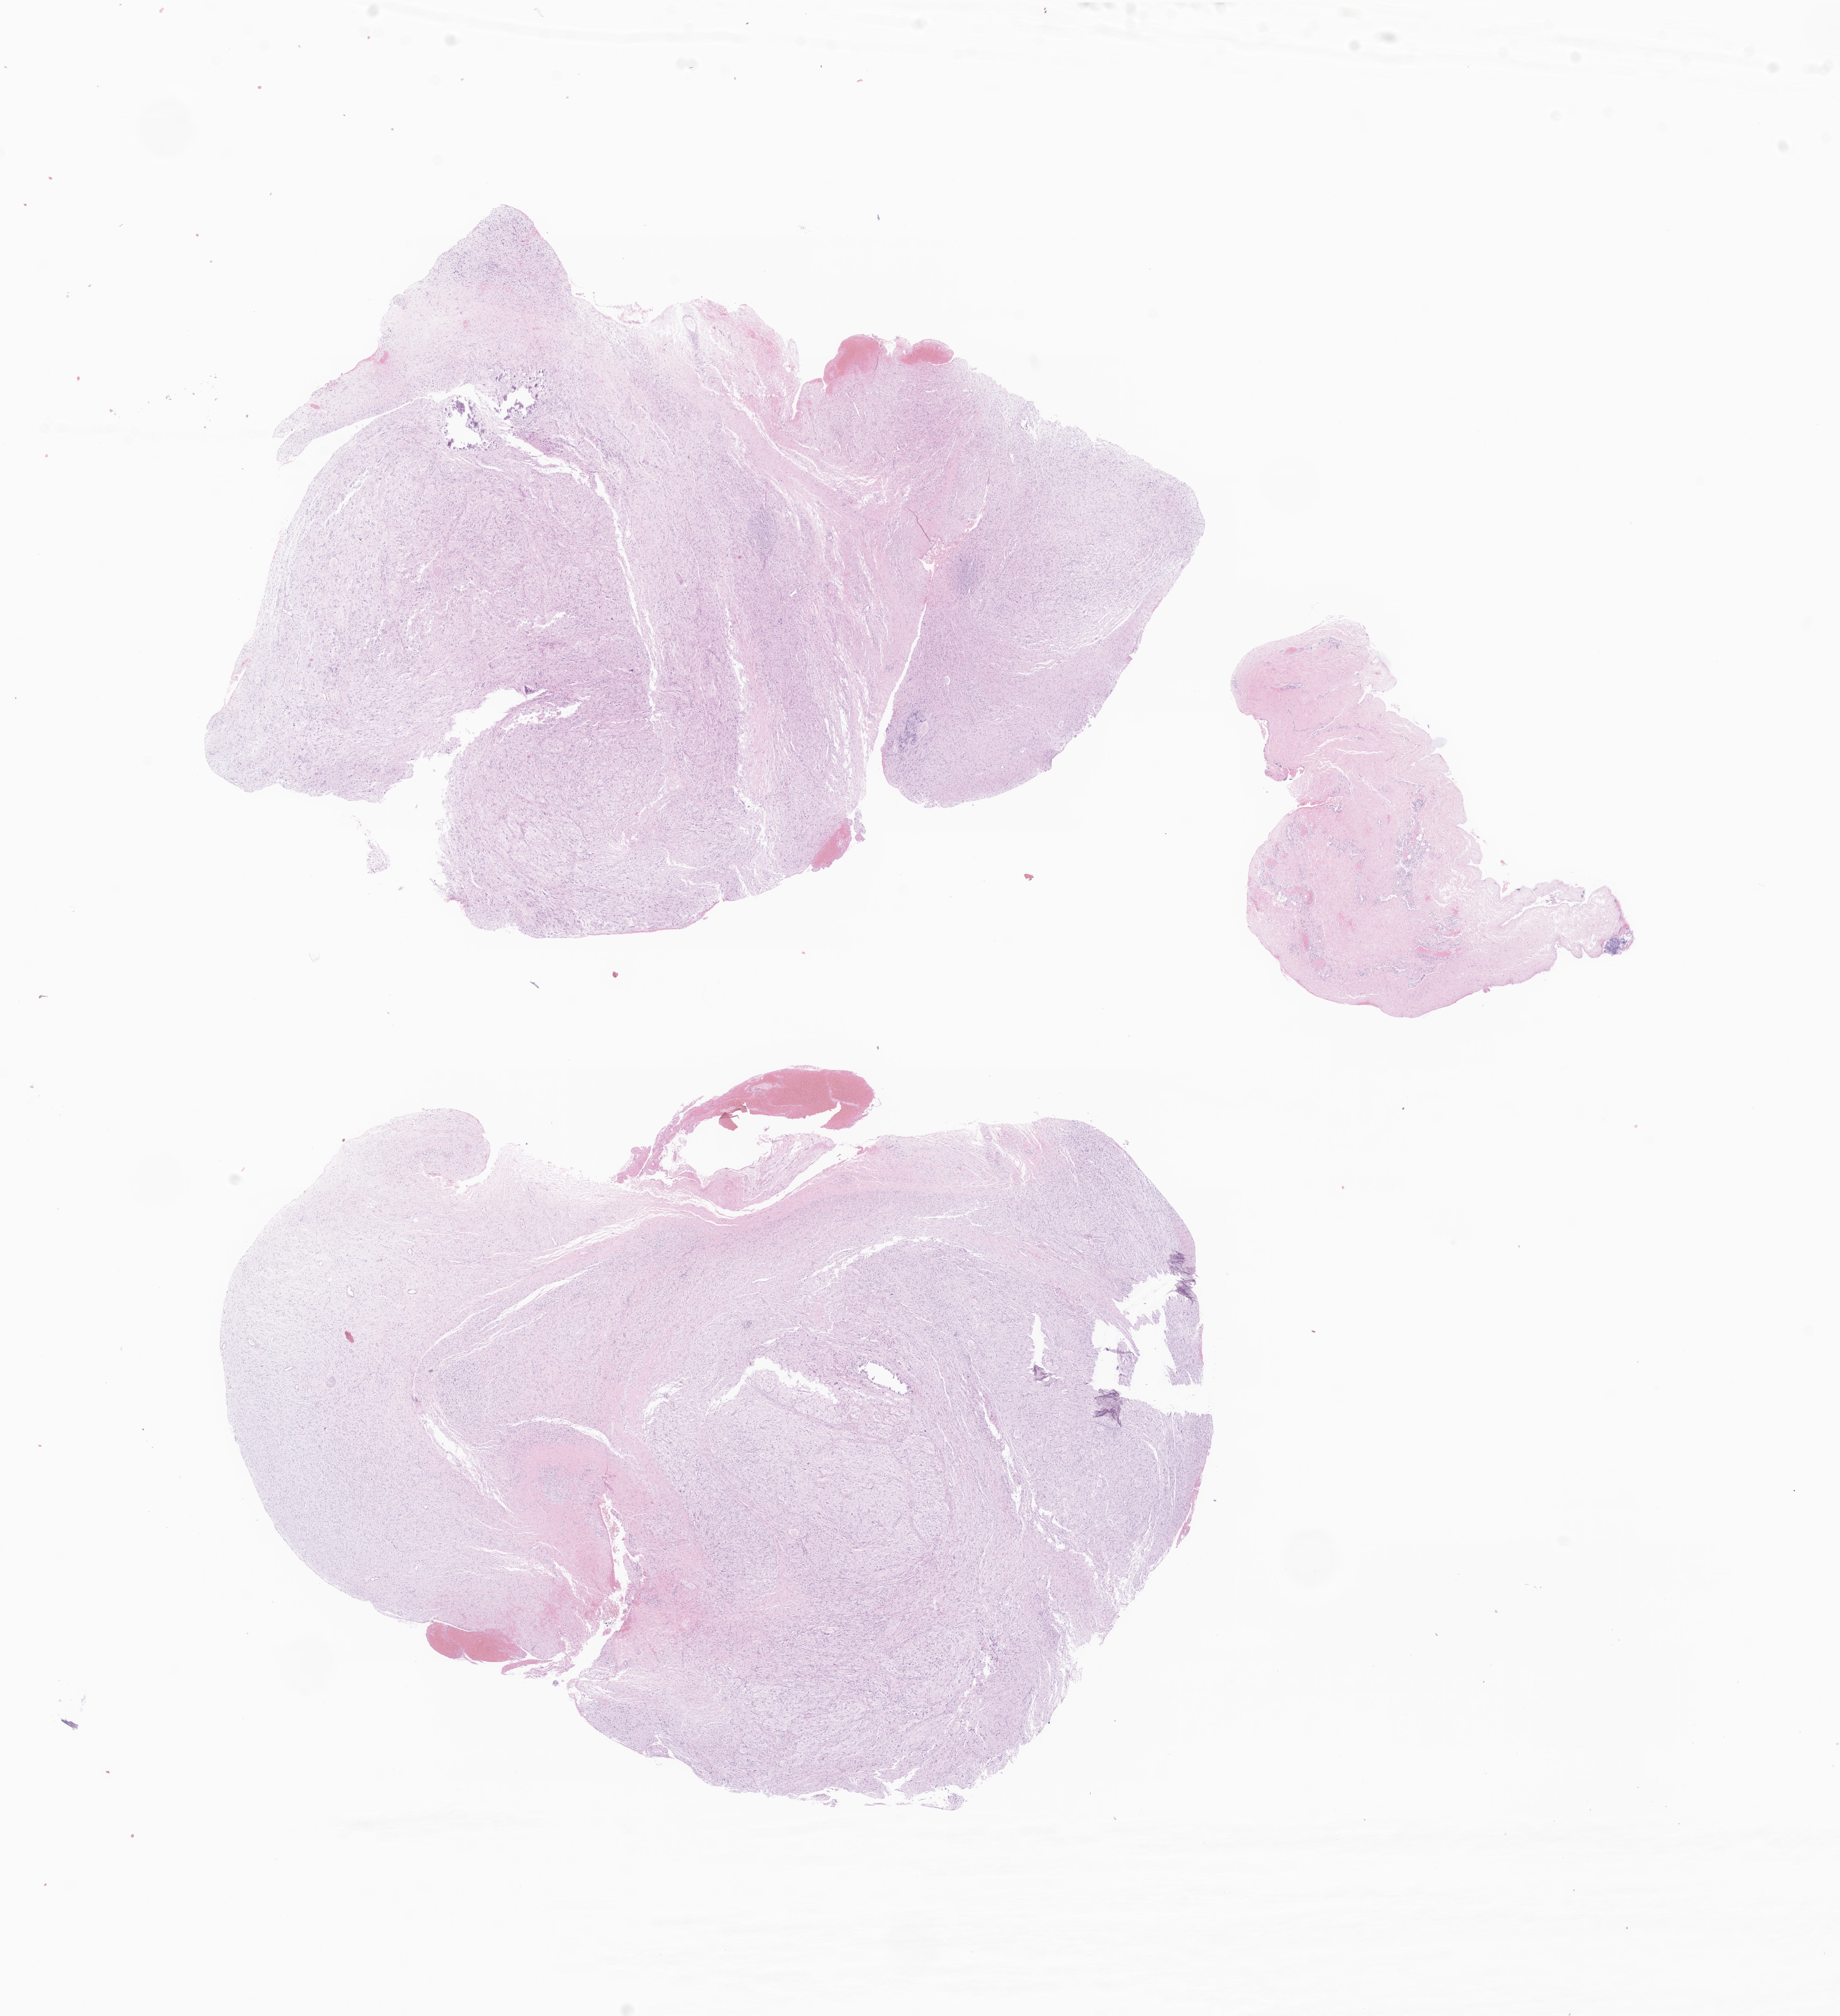
Digitized H&E-stained section of tumor tissue from the posterior mediastinum — low-resolution overview of the scanned area, about 16.5 x 18.1 mm. Formalin-fixed, paraffin-embedded (FFPE) tissue. Patient female; age 944 days (about 2.6 years).
* recorded diagnosis: Neuroblastoma, NOS